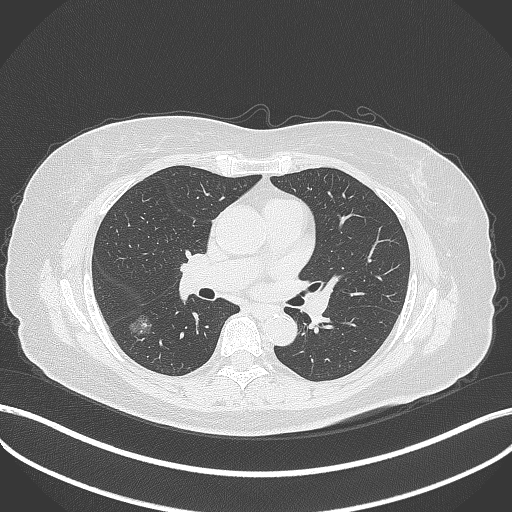
Chest CT, one axial slice; position 174 of 322 along the scan axis; reconstruction kernel B70f; 120 kVp; lung window (W 1500 / L -600 HU); 512 × 512 image matrix. Female patient, age 64 years. From the clinical record (not read from this slice): clinical TNM (as recorded): T1c N0 M0; histopathological grade: G1.
Annotated regions visible in this slice (rectangle marked by the reading radiologist):
- lung tumour (recorded histology: adenocarcinoma): bounding box <126,308,153,346> (left, top, right, bottom; pixels)